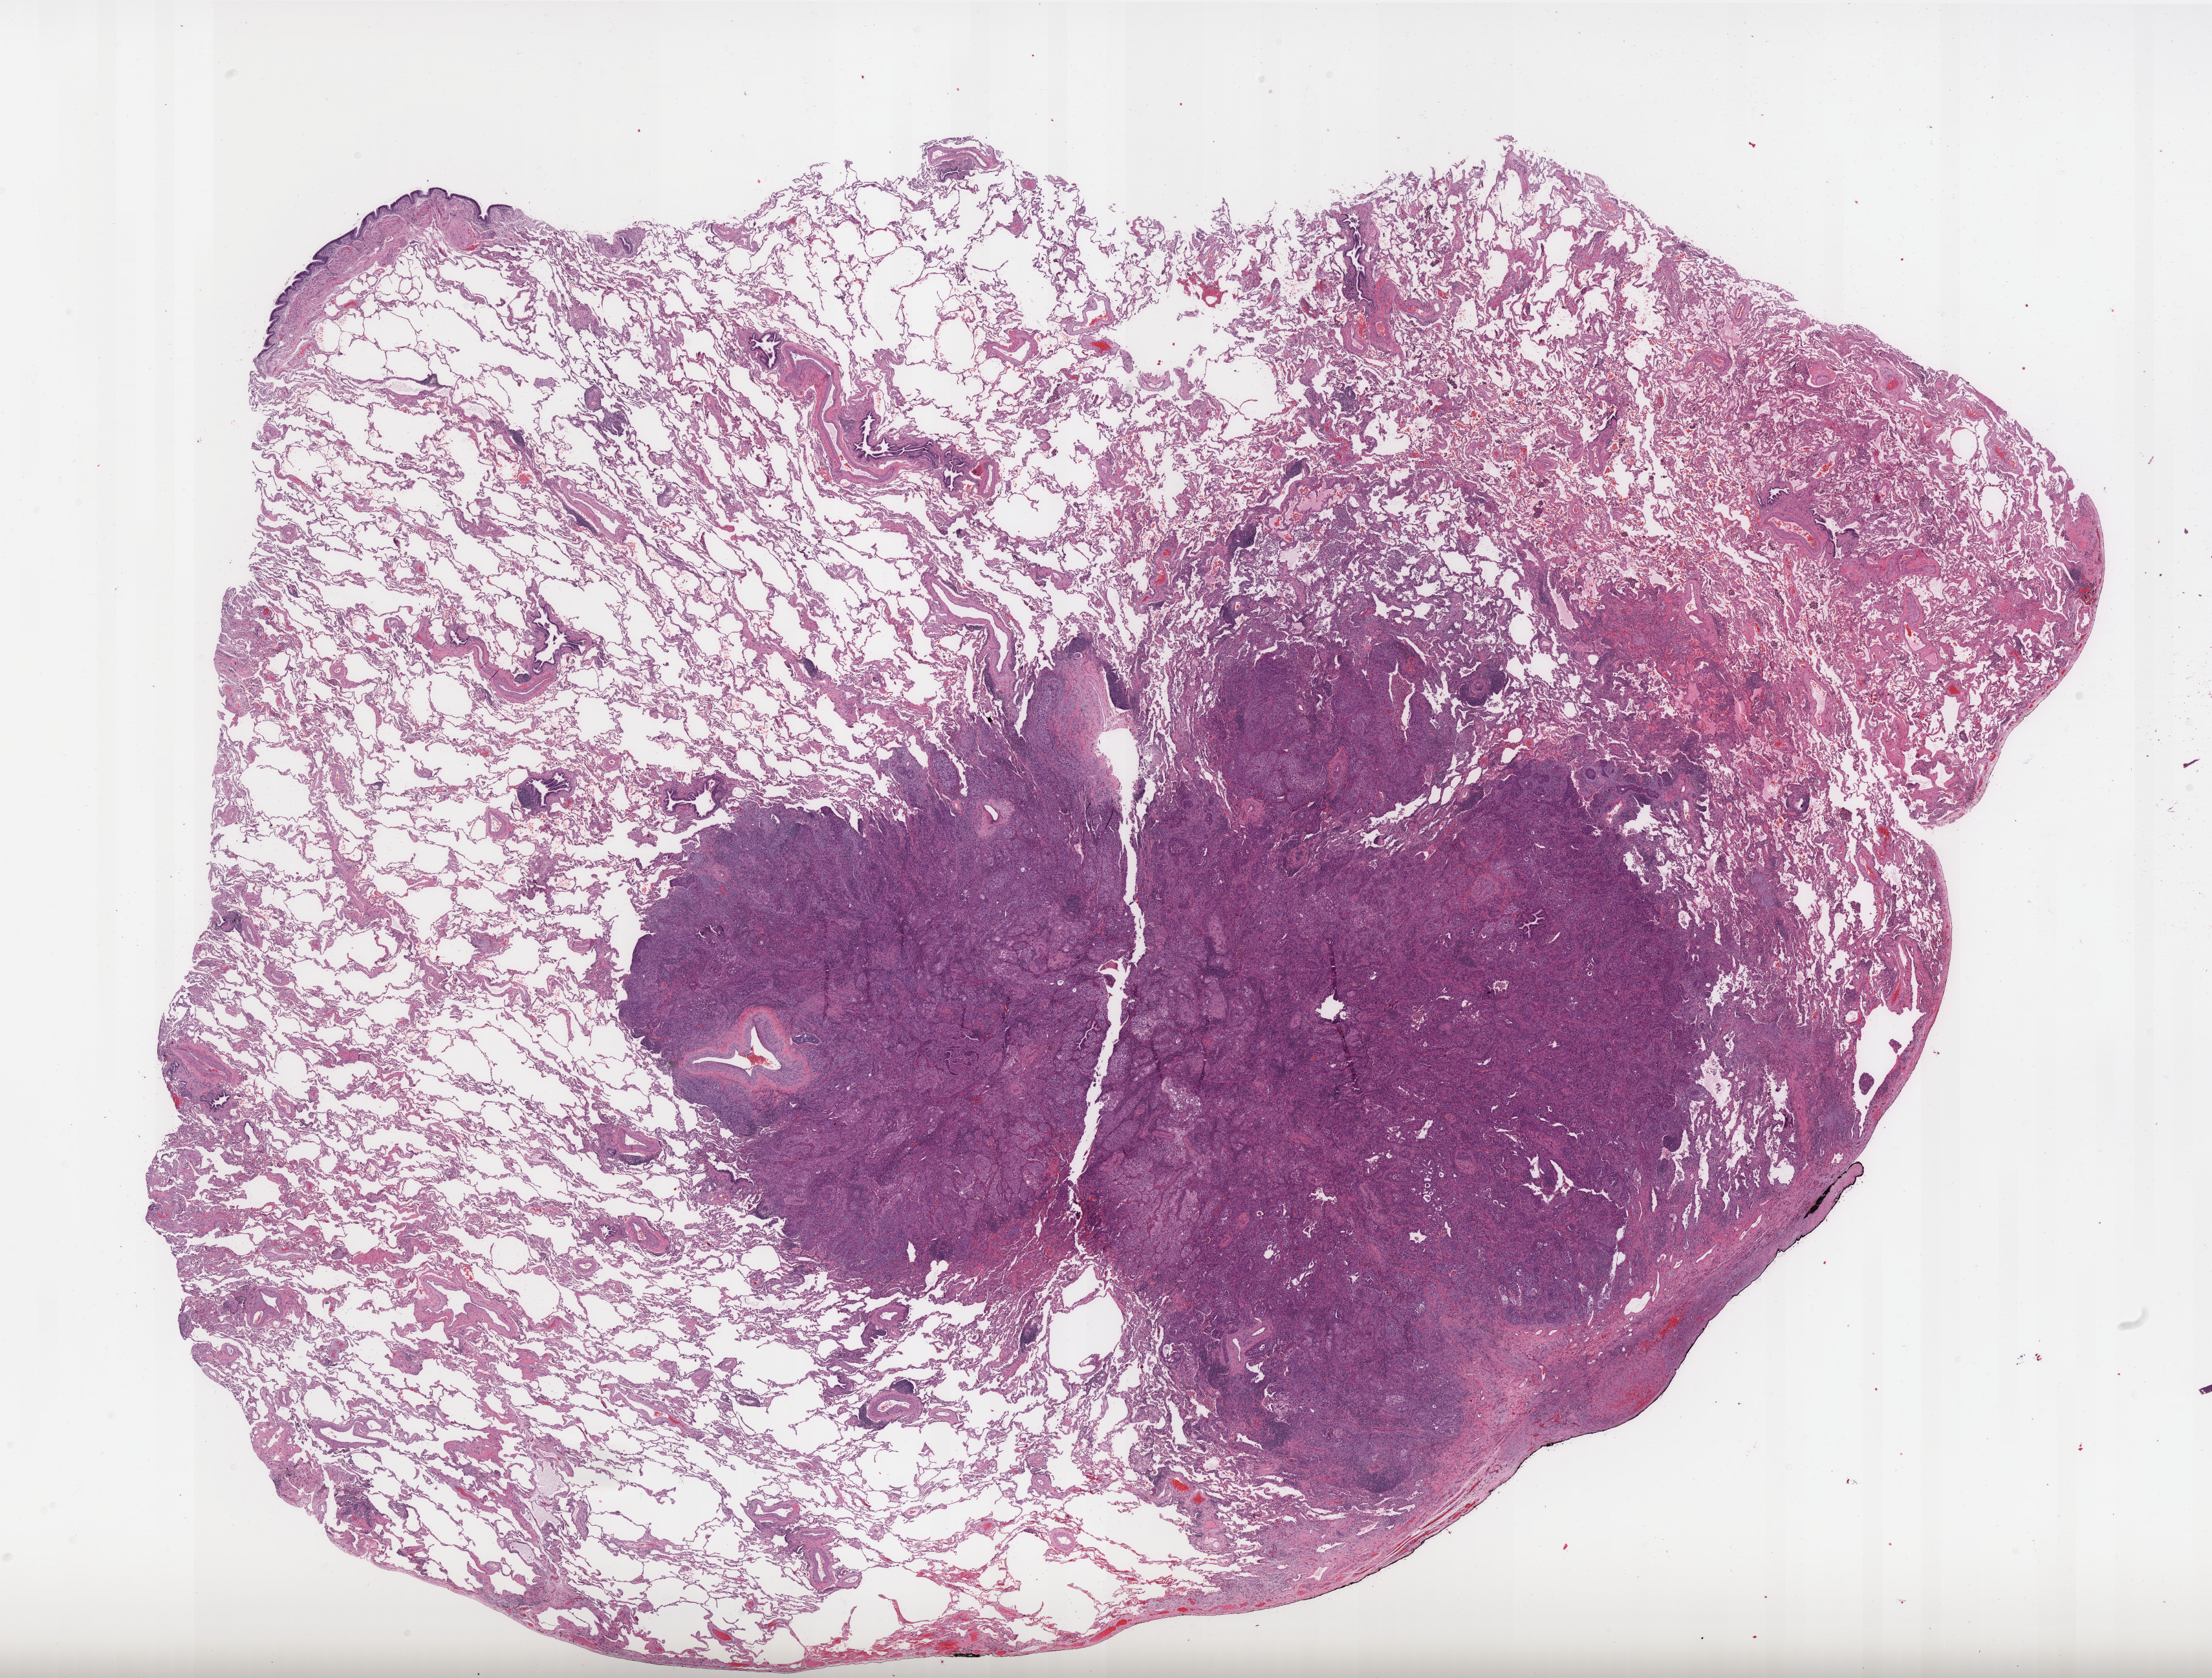
Digitized Hematoxylin and eosin (H&E) stained tissue section (whole slide), a low-resolution overview of the entire scanned area, about 27.4 x 20.8 mm (from a 40x scan), FFPE section, lung, primary tumour sample. Female, age 67 years at initial diagnosis.
* pathologic diagnosis: Squamous cell carcinoma, NOS (lower lobe, lung)
* laterality: right
* AJCC pathologic stage: IA